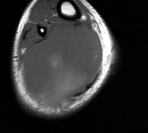
MRI of an extremity soft-tissue mass, one axial slice. MR volume resampled by the dataset authors to the PET/CT grid (not the native acquisition matrix). 3.27 mm slice thickness. 148 × 133 image matrix, field of view 145 × 130 mm. Male patient. From the clinical record (not read from this slice): histological type: liposarcoma - round cell; grade: high; site of the primary tumour: right calf.
Structures marked on this image (expert contour drawn on MRI and transferred to this co-registered scan by the dataset authors):
- gross tumour volume (mass): box from (x=22, y=26) to (x=101, y=111) px